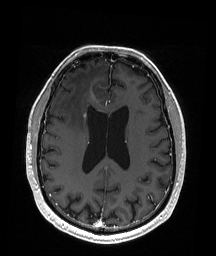
Brain MRI from a brain-tumour surgery series, one axial slice; position 77 of 192 along the scan axis; T1-weighted post-contrast; 216 × 256 image matrix. From the clinical record (not read from this slice): histopathology: Astrocytoma; WHO grade: 3; IDH mutation: yes.
Annotated regions visible in this slice (outlined manually by an expert reader):
- tumour: bounding box [x1, y1, x2, y2] px = [92, 95, 95, 99]